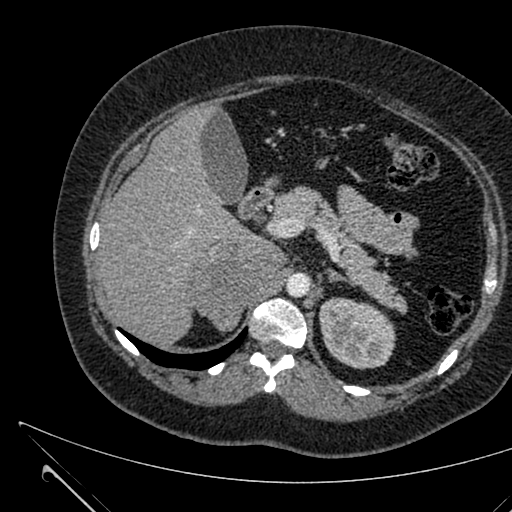
Contrast-enhanced abdominal CT, one axial slice; slice 430 of 731 in the series (ordered by position); 120 kVp; intravenous contrast given; soft-tissue window (W 400 / L 40 HU); 1 mm slice thickness; 512 × 512 image matrix. Patient: female, 36 years. From the clinical record (not read from this slice): diagnosis: adrenocortical carcinoma; tumour side: right adrenal; tumour size at pathology: 10 cm; Ki-67 index: 20 %; stage (as recorded): 4.
Outlined on this slice (semi-automatic segmentation, software-assisted and operator-edited):
- mass: box from (x=196, y=238) to (x=284, y=331) px